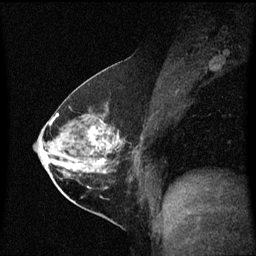
Breast MRI (dynamic contrast-enhanced), one sagittal slice; slice 29 of 60 in the series (ordered by position); dynamic contrast-enhanced series, image 2 of 3 at this slice position (ordered by acquisition); 1.5 T; TE 4.2 ms, TR 8.4 ms; 2 mm slice thickness; 256 × 256 image matrix, field of view 210 × 210 mm. Female patient, age 54 years. From the clinical record (not read from this slice): setting: breast cancer imaged before/during neoadjuvant chemotherapy; receptor status: HER2-positive.
Annotated regions visible in this slice (semi-automatic segmentation, software-assisted and operator-edited):
- analysis volume of interest (the breast-tissue region the enhancement analysis was run in; not a lesion): box from (x=59, y=115) to (x=141, y=199) px
- tumour enhancement mask (voxels above the 70 % enhancement threshold inside the analysis volume of interest): (x=64, y=127)–(x=120, y=174)